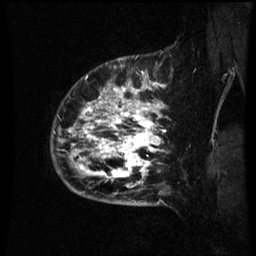
Breast MRI (dynamic contrast-enhanced), one sagittal slice; position 55 of 60 along the scan axis; dynamic contrast-enhanced series, image 2 of 3 at this slice position (ordered by acquisition); 1.5 T; TE 4.2 ms, TR 8.9 ms; 2.1 mm slice thickness; 256 × 256 image matrix, field of view 200 × 200 mm. Patient: female, 42 years. From the clinical record (not read from this slice): setting: breast cancer imaged before/during neoadjuvant chemotherapy; receptor status: HER2-positive.
Outlined on this slice (semi-automatically segmented with operator editing):
- analysis volume of interest (the breast-tissue region the enhancement analysis was run in; not a lesion): bounding box (x1, y1, x2, y2) in pixels: (66, 82, 167, 193)
- tumour enhancement mask (voxels above the 70 % enhancement threshold inside the analysis volume of interest): (70, 84, 163, 187)